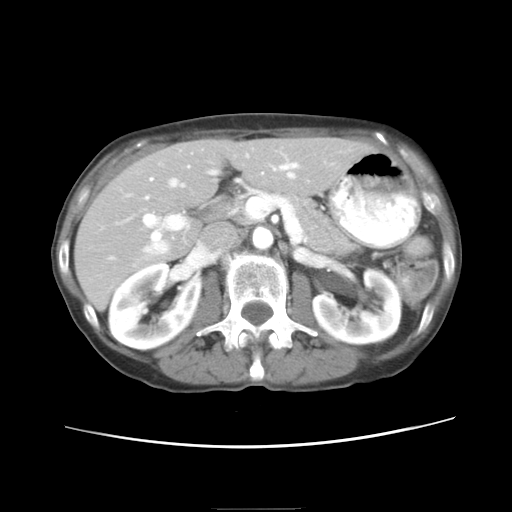
Contrast-enhanced abdominal CT, one axial slice; position 11 of 26 along the scan axis; 120 kVp; soft-tissue window (W 400 / L 40 HU); 7.5 mm slice thickness; 512 × 512 image matrix, field of view 340 × 340 mm. Female patient, age 65 years. Case-level facts recorded for this patient, not image findings: diagnosis: colorectal cancer liver metastases, imaged before liver resection; multiple liver metastases: no; disease in both lobes: yes.
Outlined on this slice (manually delineated by an expert):
- hepatic veins: box from (x=148, y=154) to (x=294, y=253) px
- liver: (x=75, y=140)–(x=365, y=304)
- planned liver remnant (the part of the liver to remain after resection): (x=76, y=140)–(x=365, y=305)
- portal vein (with intrahepatic branches): (x=143, y=163)–(x=297, y=253)